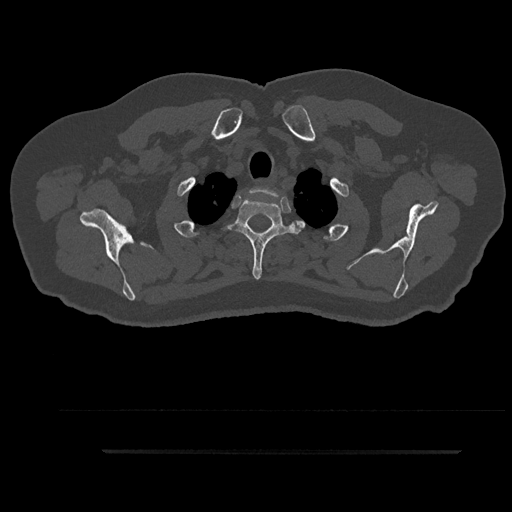
CT including the spine, one axial slice; position 759 of 797 along the scan axis; reconstruction kernel Br40s/3; 120 kVp; bone window (W 1800 / L 400 HU); 0.5 mm slice thickness; 512 × 512 image matrix. Patient: male, 63 years. From the clinical record (not read from this slice): primary cancer: renal.
Outlined on this slice (semi-automatic segmentation, software-assisted and operator-edited):
- T1 vertebra: bounding box [x1, y1, x2, y2] px = [250, 187, 284, 210]
- T2 vertebra: [227, 198, 304, 280]
- T3 vertebra: [219, 245, 293, 249]